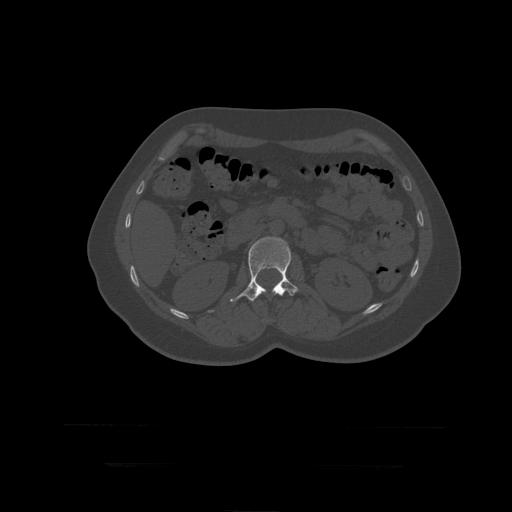
CT including the spine, one axial slice; position 151 of 399 along the scan axis; 120 kVp; bone window (W 1800 / L 400 HU); 512 × 512 image matrix, field of view 450 × 450 mm. Patient age 41 years. Case-level facts recorded for this patient, not image findings: primary cancer: breast.
Outlined on this slice (semi-automatically segmented with operator editing):
- L2 vertebra: bounding box [x1, y1, x2, y2] px = [230, 237, 299, 302]